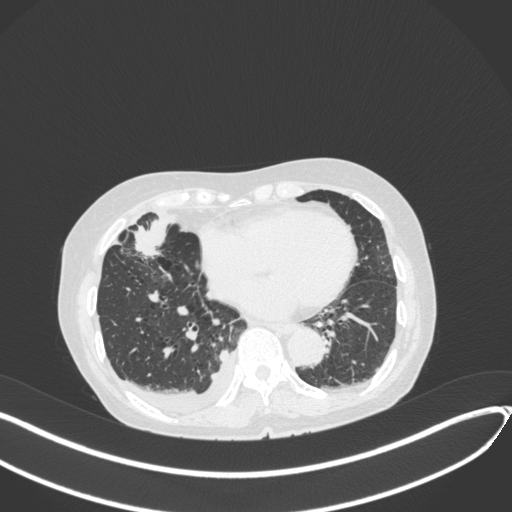
Chest CT, one axial slice. Position 136 of 418 along the scan axis. Reconstruction kernel B31f. 120 kVp. Lung window (W 1500 / L -600 HU). 1 mm slice thickness. 512 × 512 image matrix. Patient: female, 75 years. From the clinical record (not read from this slice): clinical TNM (as recorded): T2a N3 M0.
Structures marked on this image (rectangle marked by the reading radiologist):
- lung tumour (recorded histology: adenocarcinoma): bounding box [x1, y1, x2, y2] px = [130, 212, 177, 263]